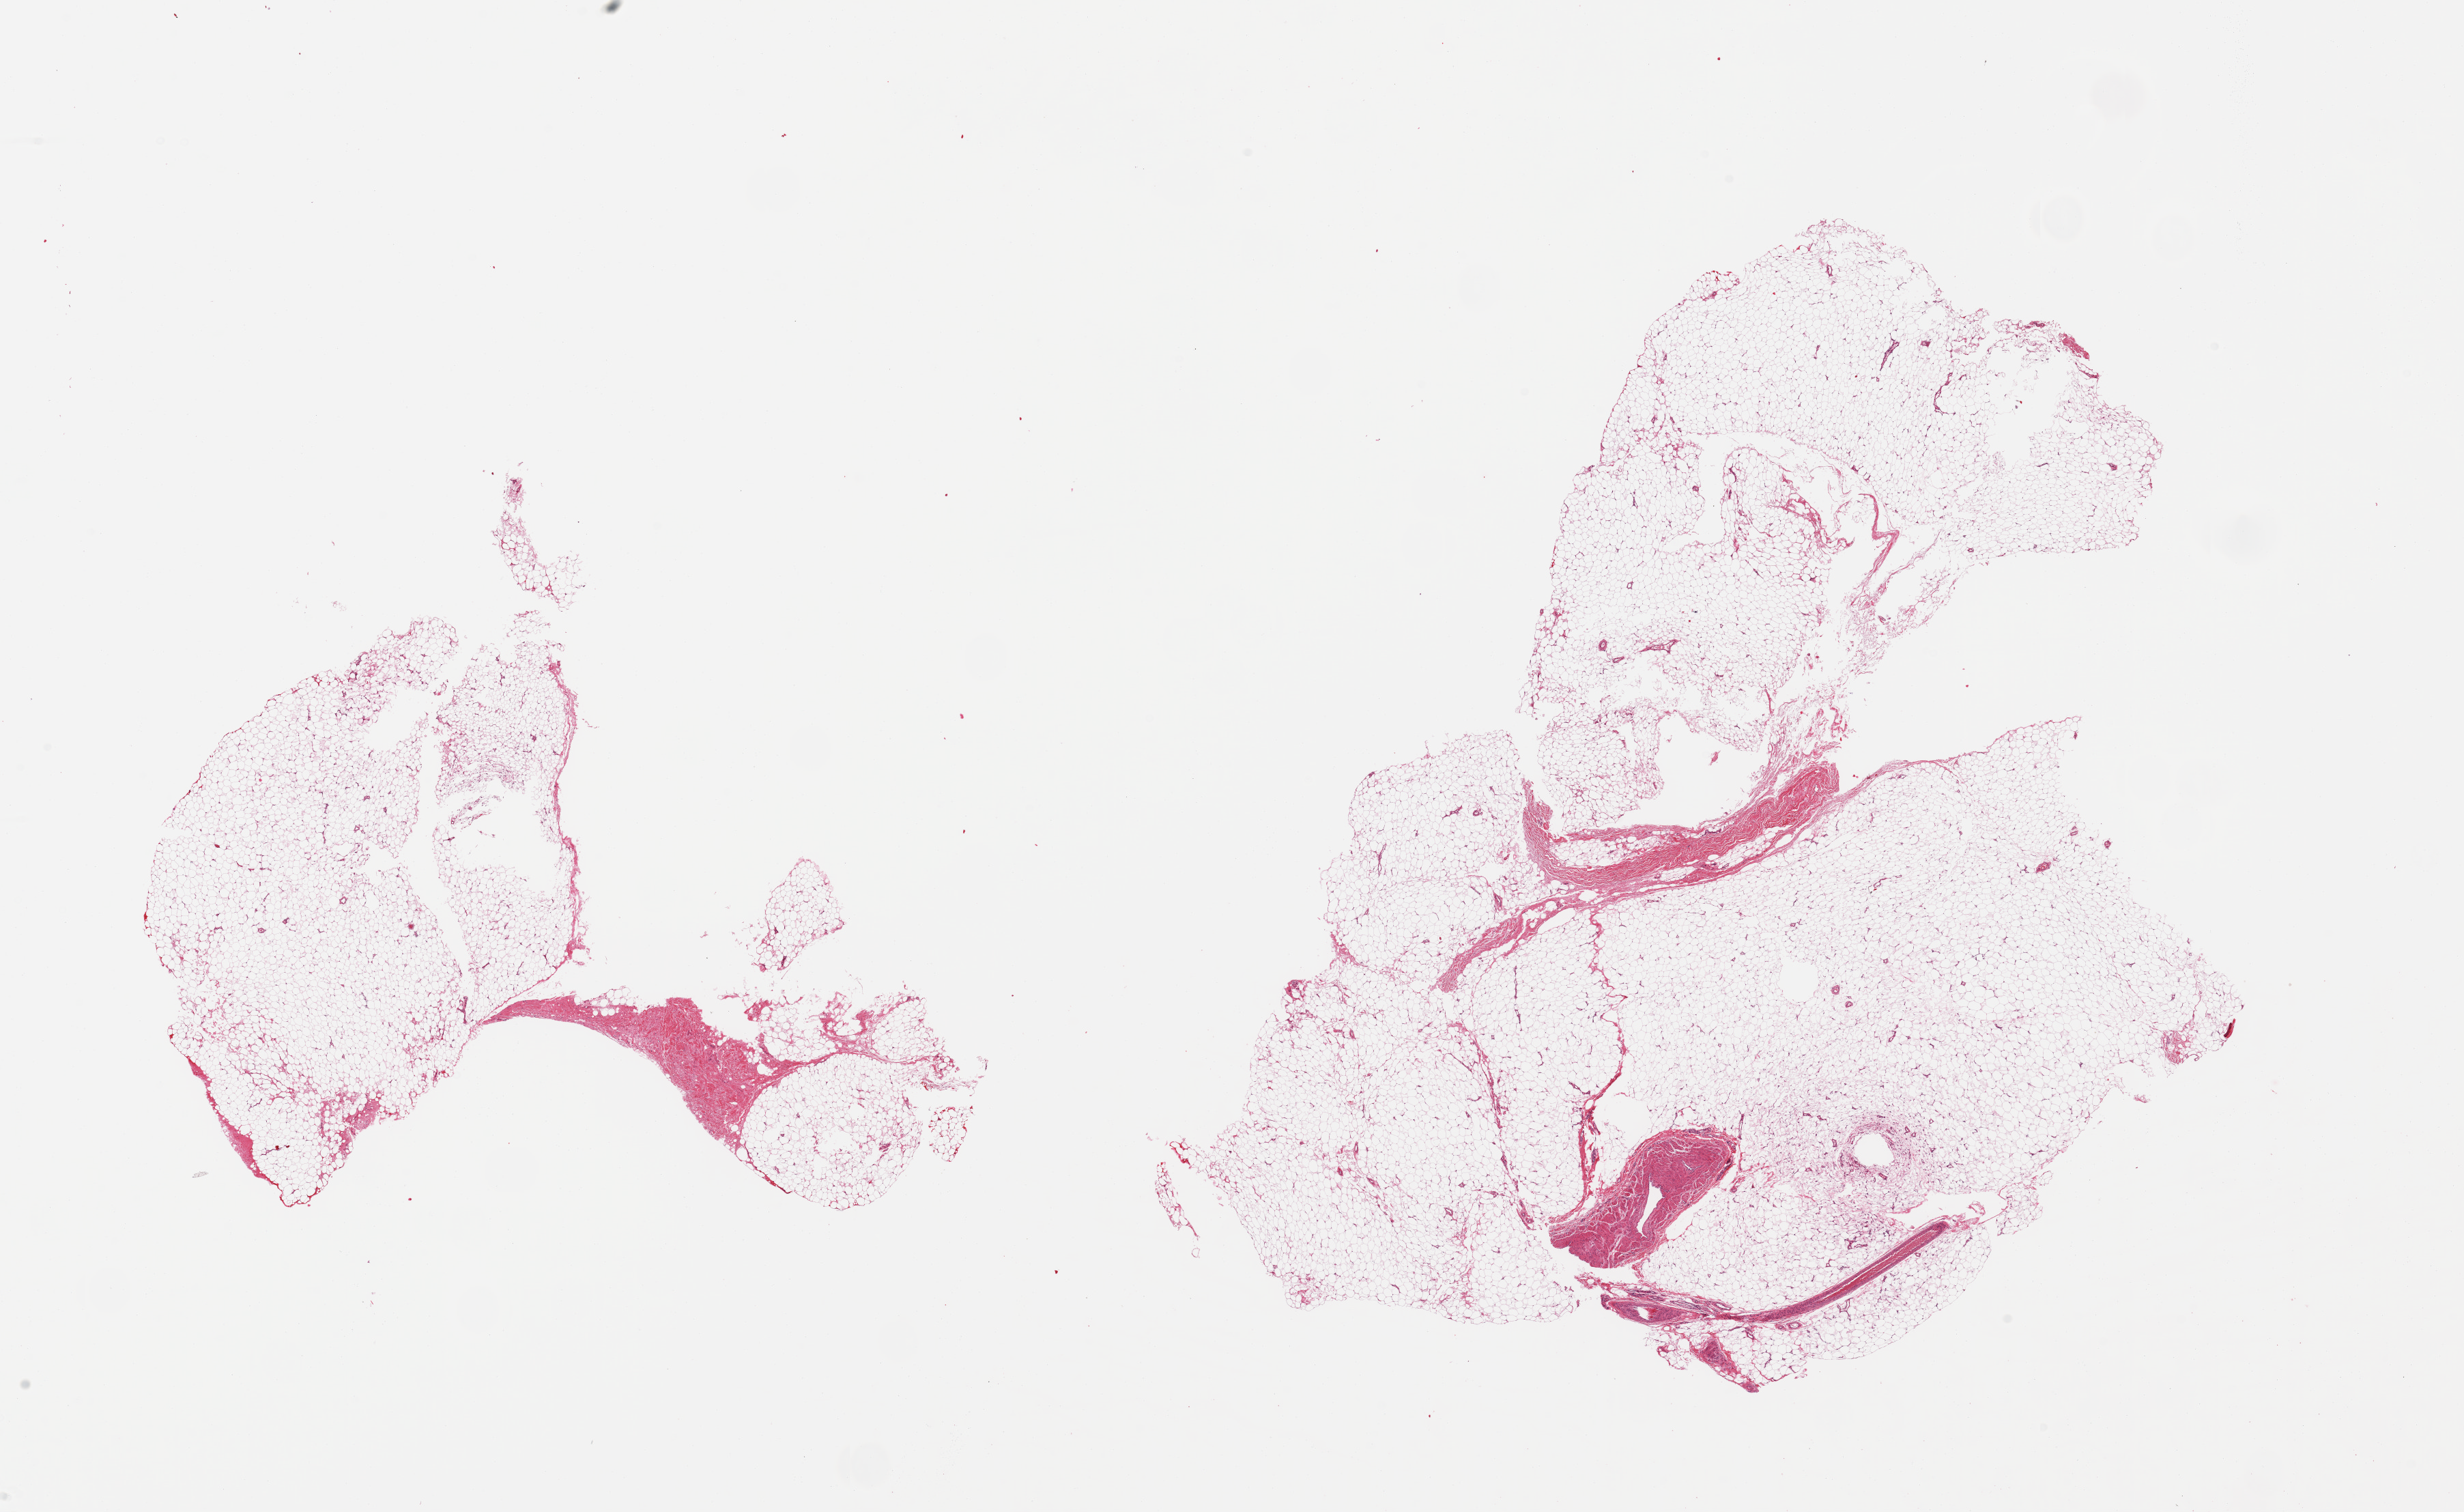
Whole-slide image, H&E stain, low-resolution overview of the scanned area, about 28.5 x 17.5 mm (slide scanned at 20x), PAXgene-fixed, paraffin-embedded tissue, target tissue: adipose tissue, tissue donor sample. Female donor.
Pathologist's review note for this sample: 2 pieces; mature adipose tissue, small component of fibrous tissue and larger vessels.